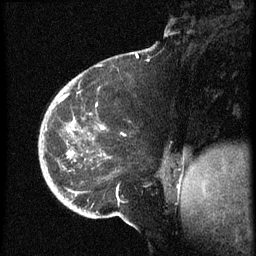
Breast MRI (dynamic contrast-enhanced), one sagittal slice; slice 19 of 60 in the series (ordered by position); dynamic contrast-enhanced series, image 2 of 3 at this slice position (ordered by acquisition); 1.5 T; TE 4.2 ms, TR 8.4 ms; 256 × 256 image matrix, field of view 200 × 200 mm. Female patient, age 38 years. Case-level facts recorded for this patient, not image findings: setting: breast cancer imaged before/during neoadjuvant chemotherapy; receptor status: HER2-positive.
Structures marked on this image (semi-automatically segmented with operator editing):
- analysis volume of interest (the breast-tissue region the enhancement analysis was run in; not a lesion): box from (x=39, y=74) to (x=173, y=202) px
- tumour enhancement mask (voxels above the 70 % enhancement threshold inside the analysis volume of interest): (x=60, y=97)–(x=107, y=162)